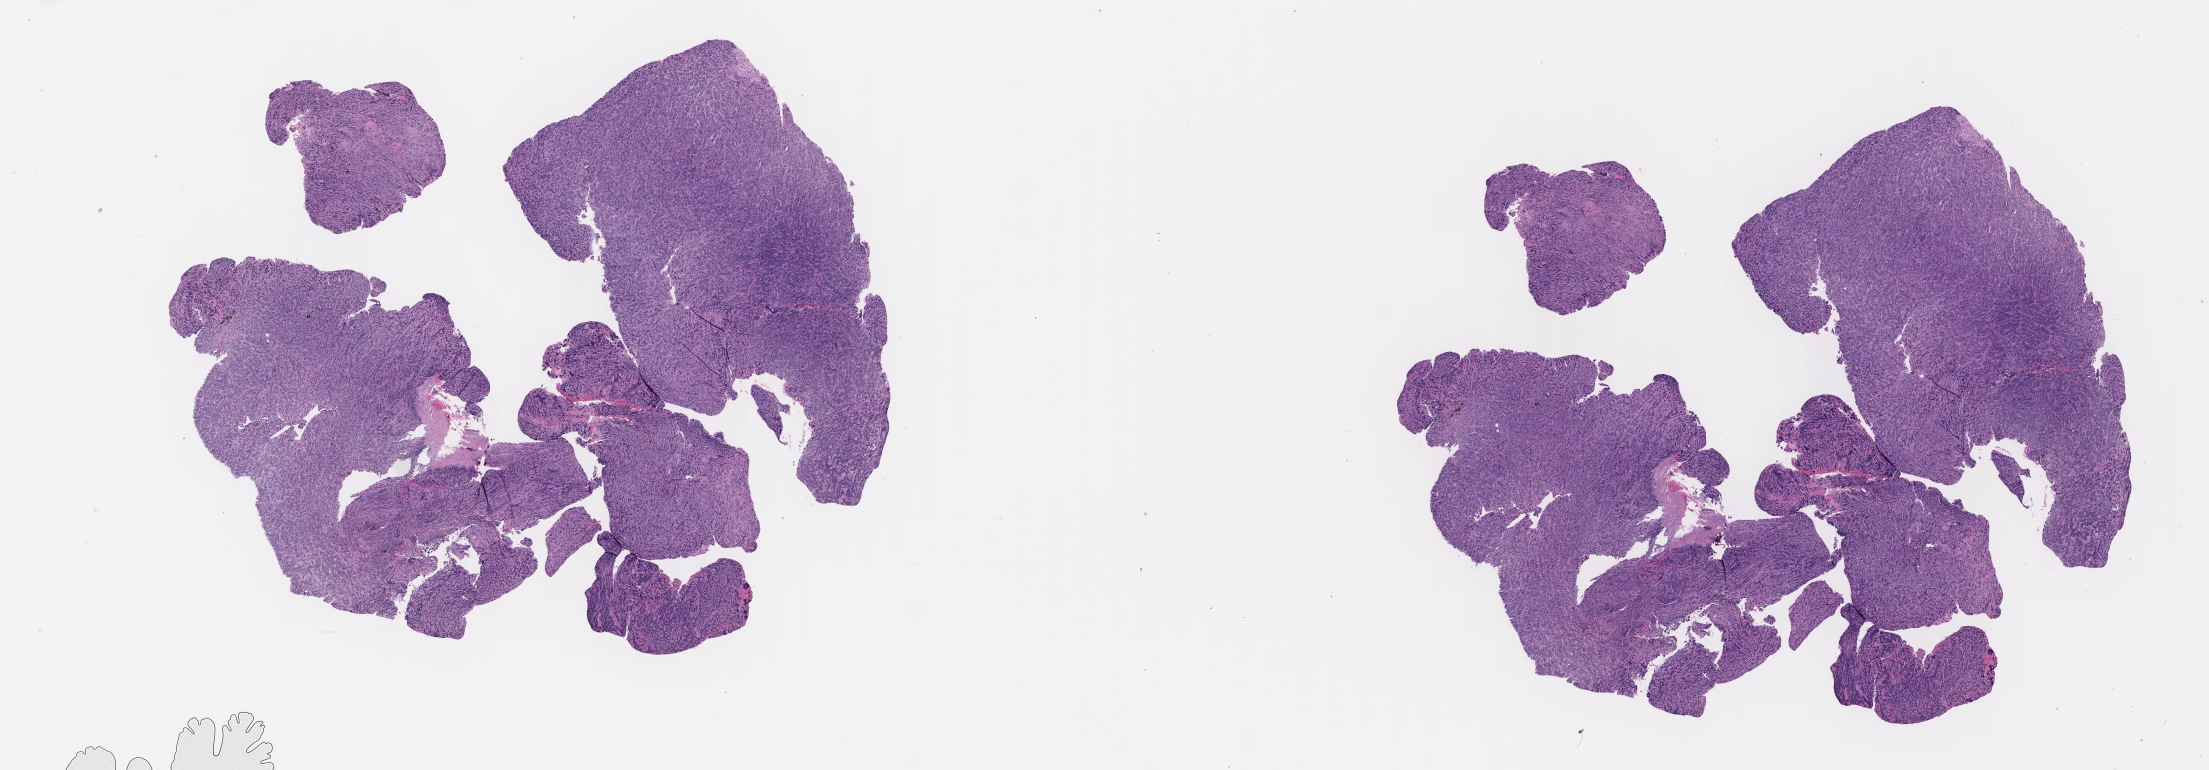
Hematoxylin and eosin (H&E) whole-slide image of tumor tissue, shown as a low-resolution overview of the whole scanned area (about 35.7 x 12.5 mm); formalin-fixed, paraffin-embedded (FFPE) tissue; site: soft tissue, cheek-left. Female patient, age at diagnosis 10.8 years.
• primary site (case record): nasopharynx
• diagnosis: rhabdomyosarcoma; histological classification: embryonal rhabdomyosarcoma
• metastatic status at presentation (as recorded): non-metastatic
• stage (as recorded): 3